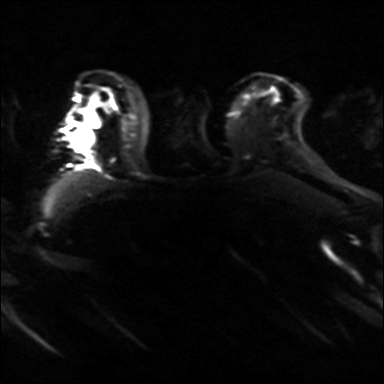
Breast MRI, one axial slice; slice 25 of 36 in the series (ordered by position); diffusion-weighted series; image 2 of 4 stored at this slice position (different b-values; order by instance number); 3 T; 4 mm slice thickness; 384 × 384 image matrix, field of view 320 × 320 mm. Female patient.
Outlined on this slice (manually delineated by an expert):
- tumour on diffusion-weighted imaging: bounding box (x1, y1, x2, y2) in pixels: (71, 115, 102, 149)